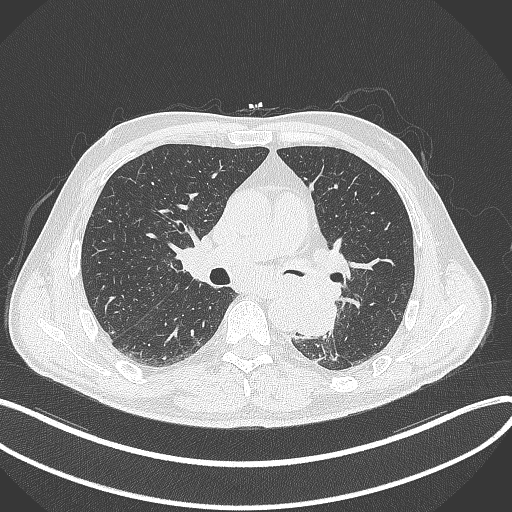
Chest CT, one axial slice. Slice 195 of 329 in the series (ordered by position). Reconstruction kernel B70f. 120 kVp. Lung window (W 1500 / L -600 HU). 1 mm slice thickness. 512 × 512 image matrix, field of view 400 × 400 mm. Patient: male, 59 years. Case-level facts recorded for this patient, not image findings: clinical TNM (as recorded): T2a N2 M0.
Structures marked on this image (bounding box drawn by a radiologist):
- lung tumour (recorded histology: squamous cell carcinoma): bounding box [x1, y1, x2, y2] px = [292, 288, 340, 341]